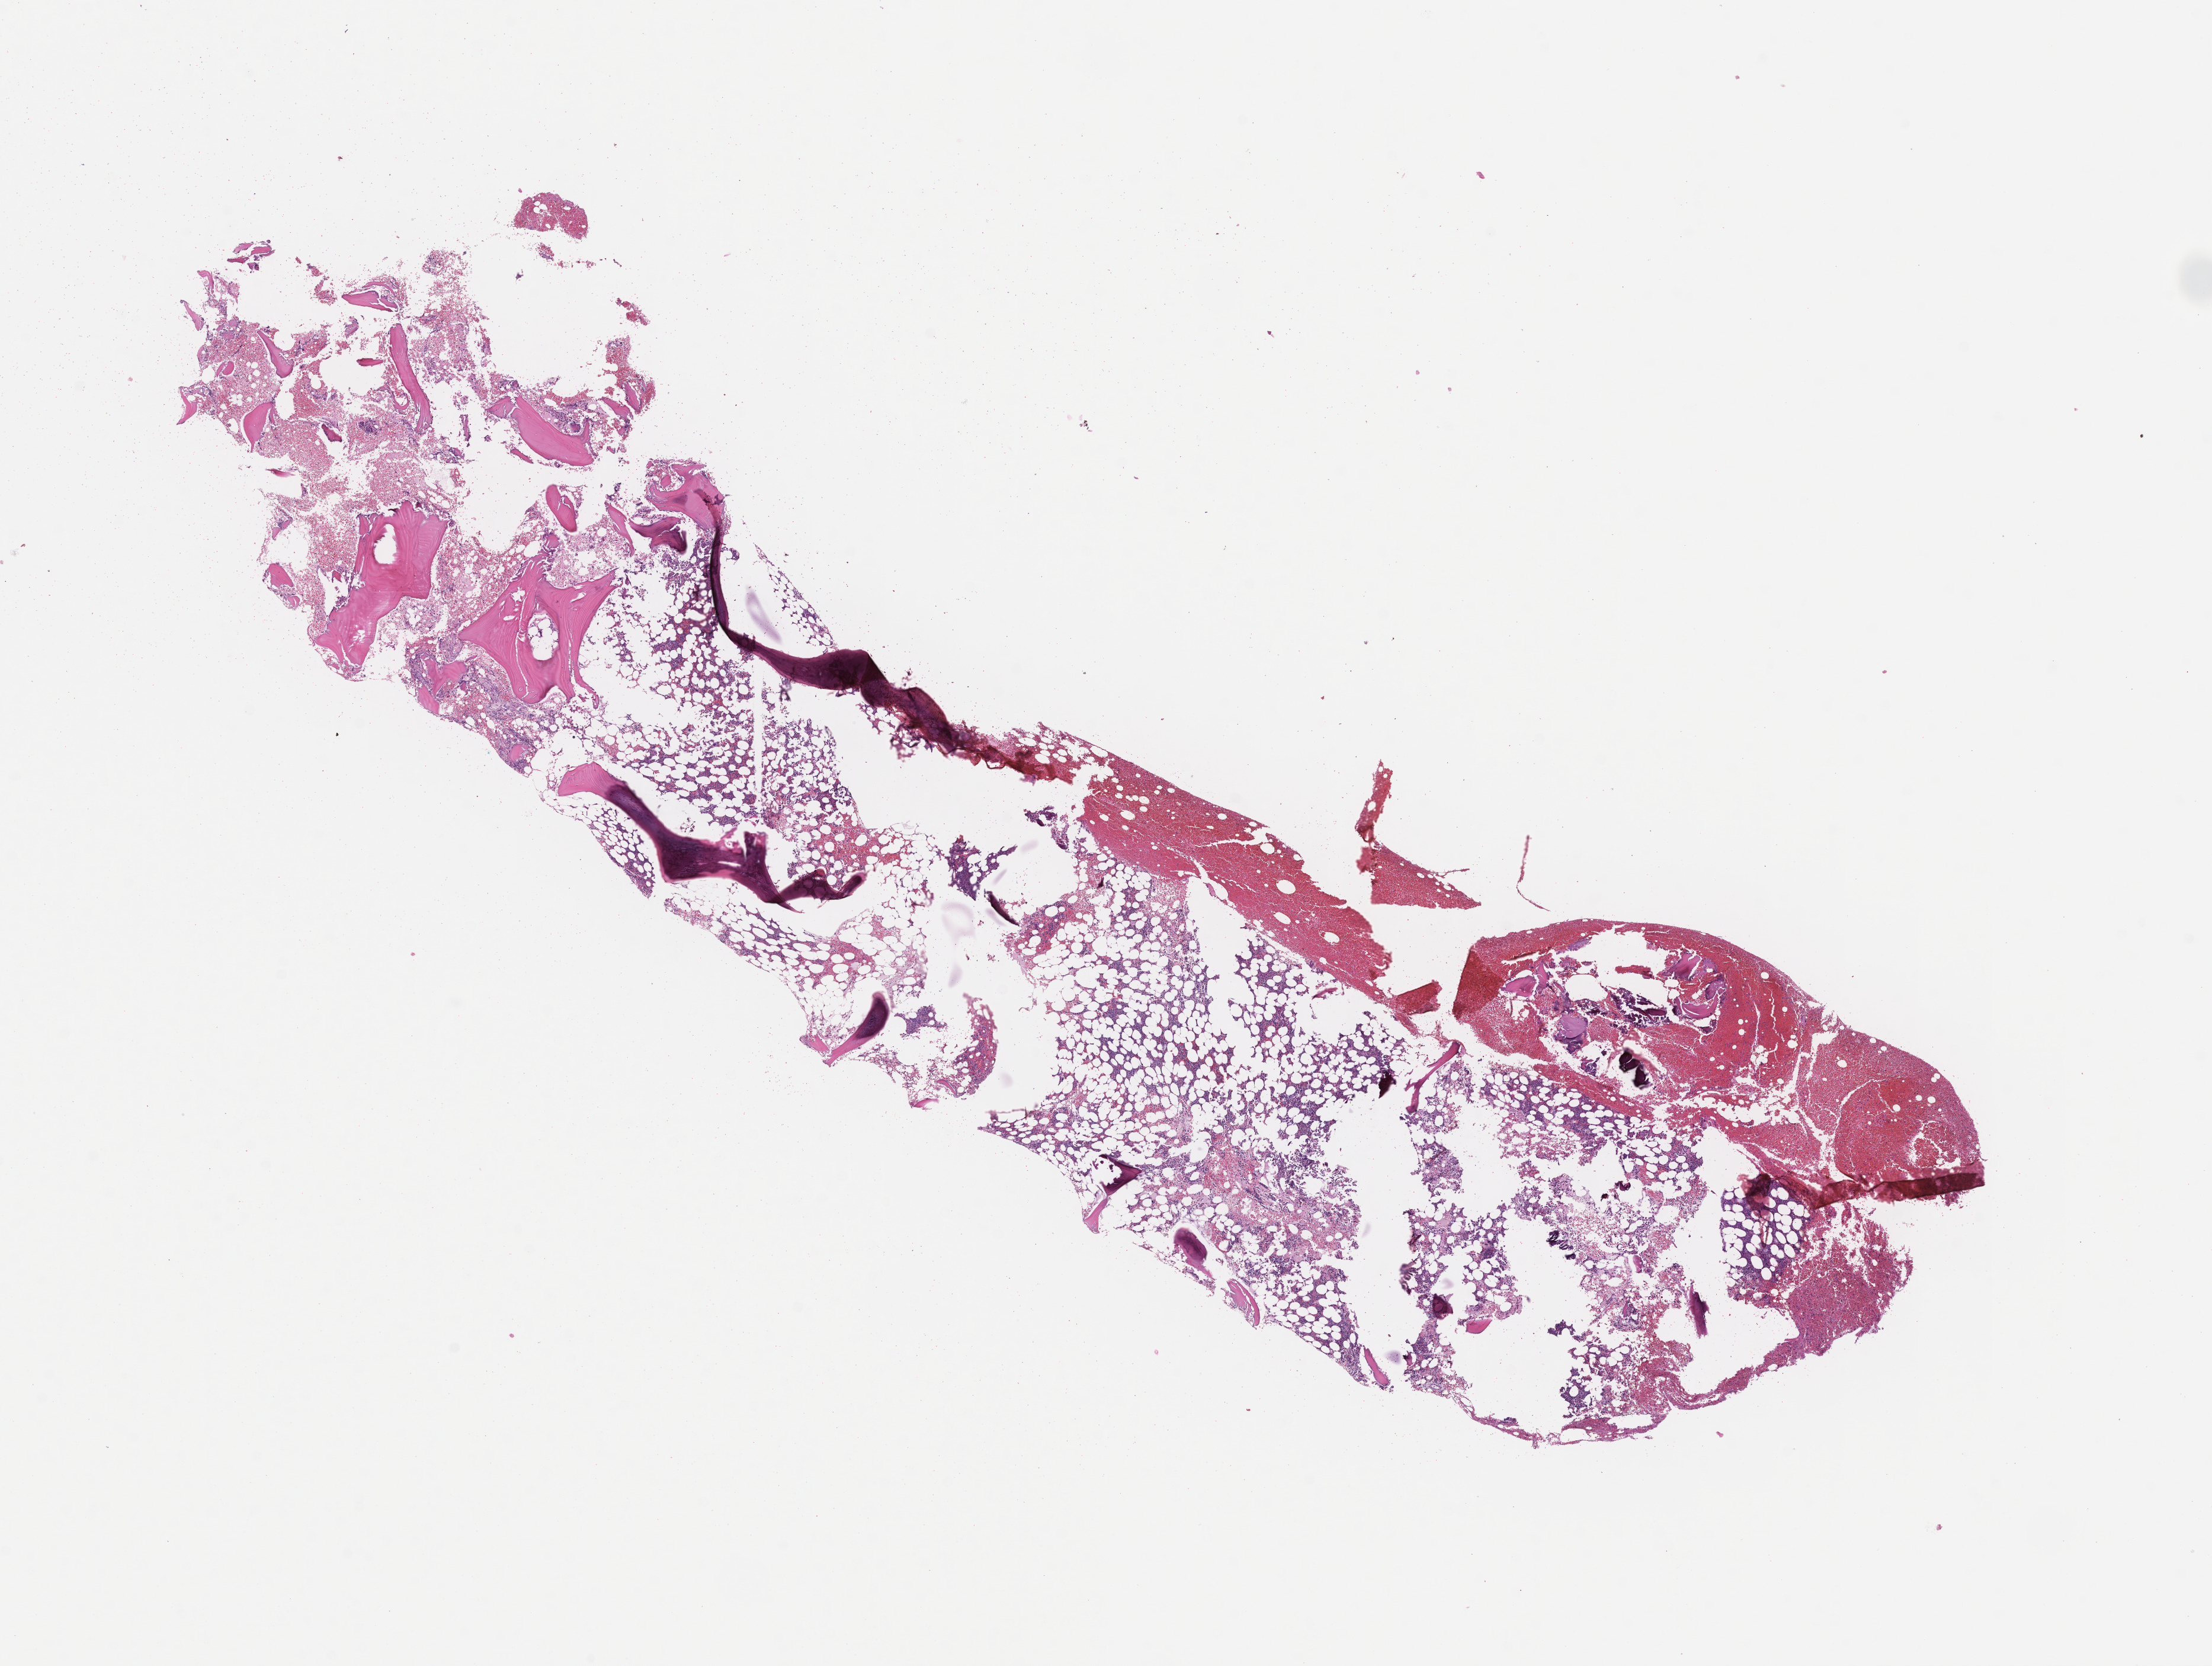
Digitized haematoxylin and eosin-stained section — a low-resolution overview of the entire scanned area, about 15.1 x 11.4 mm, FFPE section, site: bone marrow. Patient sex: female.
This section: primary tumor. Diagnosis: Plasma Cell Myeloma.